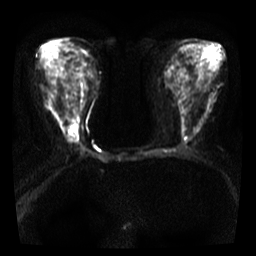
Breast MRI, one axial slice. Position 16 of 36 along the scan axis. Diffusion-weighted series; image 2 of 4 stored at this slice position (different b-values; order by instance number). 3 T. 5 mm slice thickness. 256 × 256 image matrix, field of view 300 × 300 mm. Female patient.
Outlined on this slice (manually delineated by an expert):
- tumour on diffusion-weighted imaging: bounding box <67,124,78,137> (left, top, right, bottom; pixels)